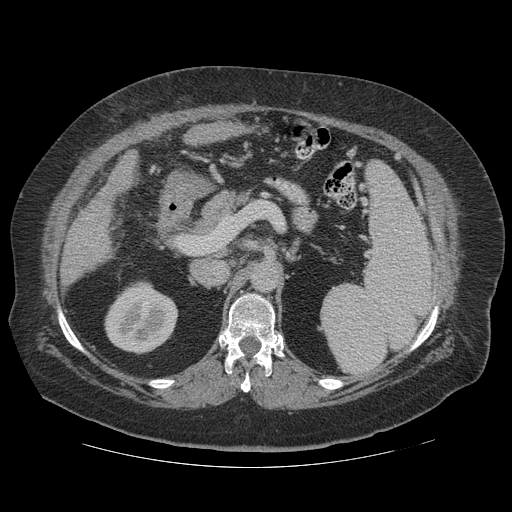
Contrast-enhanced abdominal CT (liver protocol), one axial slice. Position 60 of 121 along the scan axis. Soft-tissue window (W 400 / L 40 HU). 2.5 mm slice thickness. 512 × 512 image matrix, field of view 420 × 420 mm. From the clinical record (not read from this slice): diagnosis: hepatocellular carcinoma (patient treated with transarterial chemoembolisation; whether this scan precedes or follows treatment is not stated here); TNM stage (as recorded): Stage-IIIA; Child-Pugh class: A; tumour differentiation: well differentiated; tumour nodularity: multinodular.
Annotated regions visible in this slice (semi-automatic segmentation, software-assisted and operator-edited):
- liver parenchyma outside the tumour (the mass and vessels are separate outlines, so this box may not span the whole liver): box from (x=60, y=152) to (x=137, y=284) px